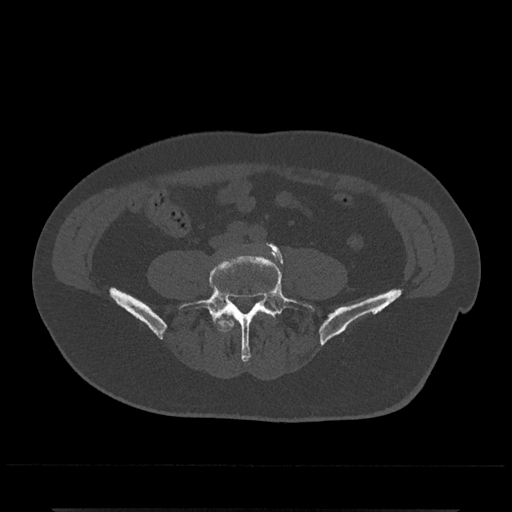
CT including the spine, one axial slice; position 101 of 797 along the scan axis; reconstruction kernel Br40s/3; bone window (W 1800 / L 400 HU); 512 × 512 image matrix, field of view 393 × 393 mm. Male patient, age 67 years. From the clinical record (not read from this slice): primary cancer: prostate.
Structures marked on this image (semi-automatic segmentation, software-assisted and operator-edited):
- L4 vertebra: bounding box <218,311,266,332> (left, top, right, bottom; pixels)
- L5 vertebra: <179,243,315,362>